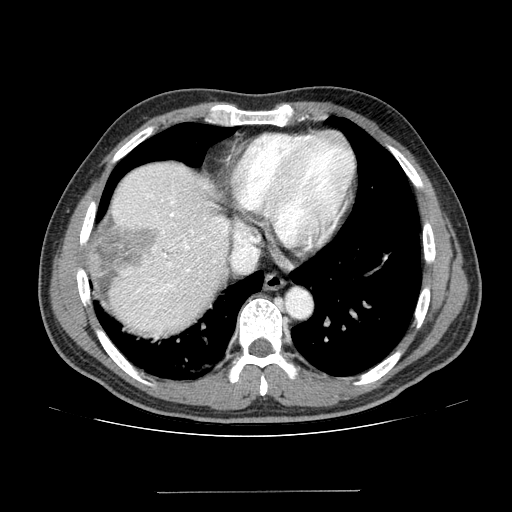
Contrast-enhanced abdominal CT (liver protocol), one axial slice; slice 117 of 131 in the series (ordered by position); 100 kVp; one of 2 acquisitions stored at this slice position; soft-tissue window (W 400 / L 40 HU); 2.5 mm slice thickness; 512 × 512 image matrix, field of view 380 × 380 mm. Case-level facts recorded for this patient, not image findings: diagnosis: hepatocellular carcinoma (patient treated with transarterial chemoembolisation; whether this scan precedes or follows treatment is not stated here); TNM stage (as recorded): Stage-I.
Annotated regions visible in this slice (semi-automatic segmentation, software-assisted and operator-edited):
- liver parenchyma outside the tumour (the mass and vessels are separate outlines, so this box may not span the whole liver): bounding box <88,162,230,336> (left, top, right, bottom; pixels)
- mass: <96,222,157,274>
- liver vessels: <114,193,228,315>